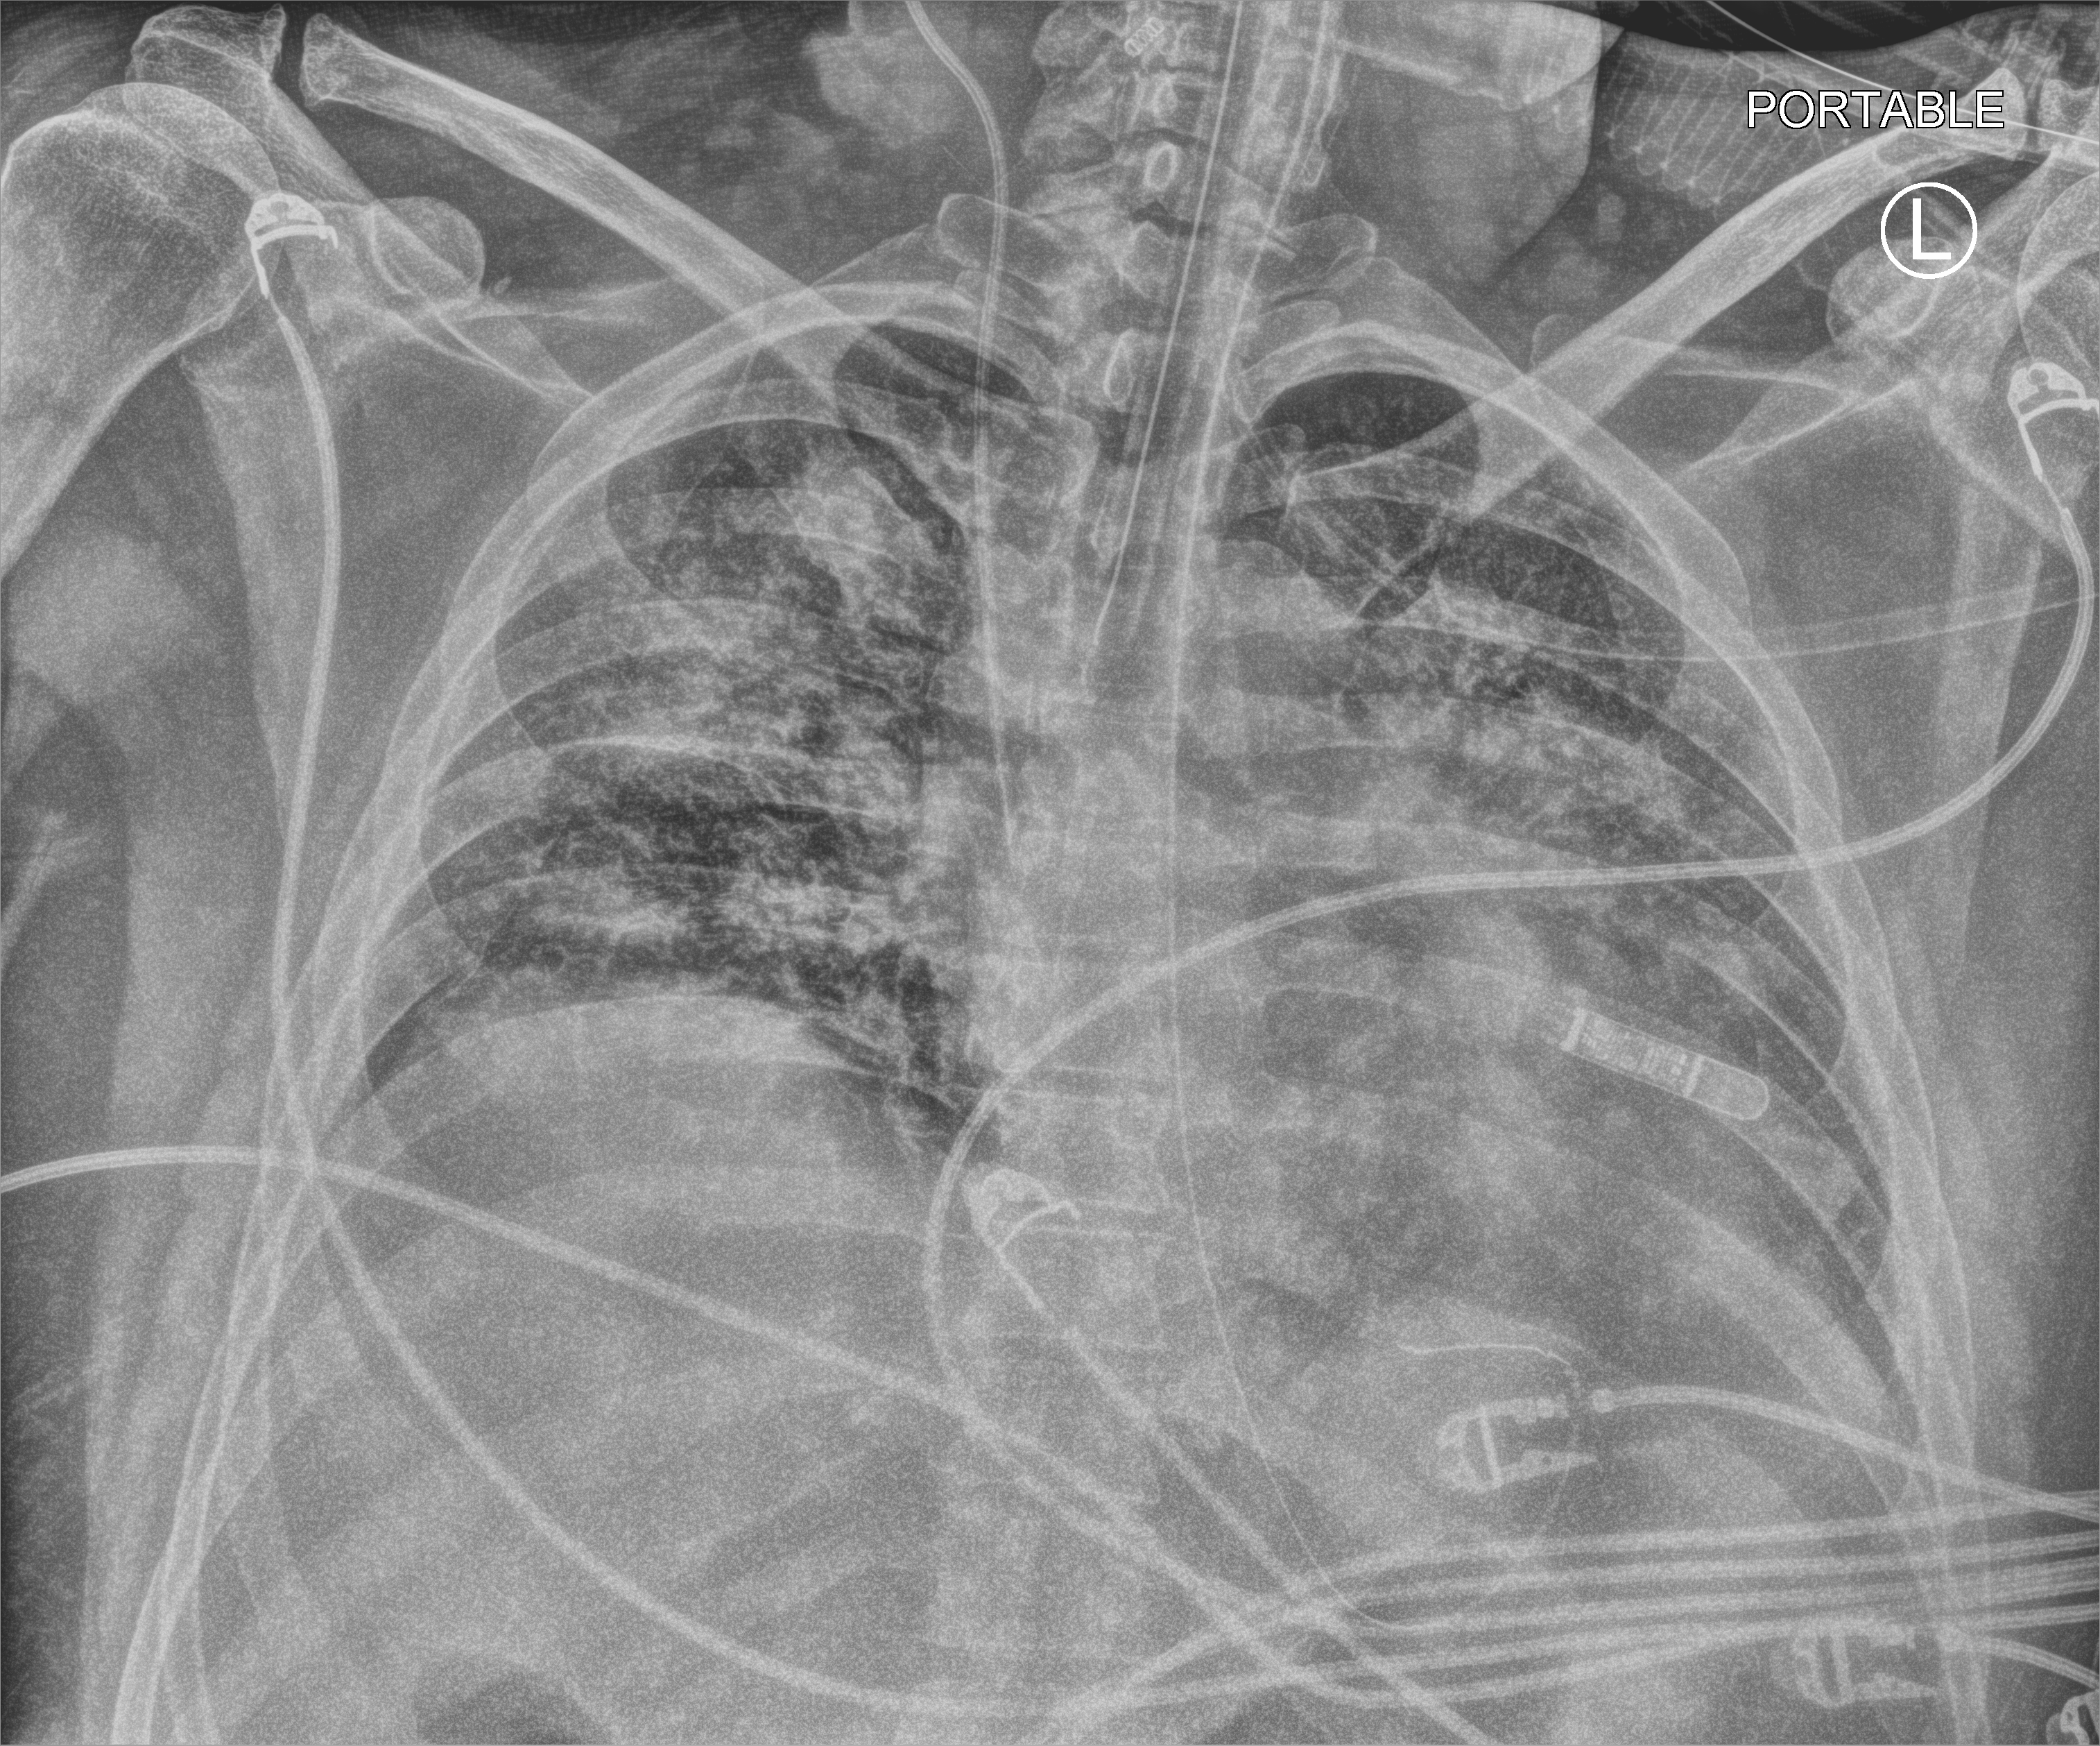
Chest X-ray (portable). Patient hospitalised with COVID-19; male, aged 18–59 years.
From the hospital-stay record, not from the radiograph (when in the stay this image was taken is not recorded):
- smoking status (admission record): former
- hypertension (admission record): yes